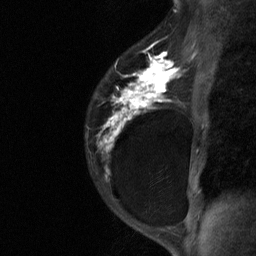
Breast MRI (dynamic contrast-enhanced), one sagittal slice. Slice 47 of 64 in the series (ordered by position). Dynamic contrast-enhanced study with each time point stored as its own series, time point 2 of 3 at this slice position (early post-contrast, ordered by acquisition time). 1.5 T. TE 4.8 ms, TR 27 ms. 2 mm slice thickness. 256 × 256 image matrix, field of view 180 × 180 mm. Female patient, age 34 years. Case-level facts recorded for this patient, not image findings: setting: breast cancer imaged before/during neoadjuvant chemotherapy; receptor status: HR-positive, HER2-negative.
Outlined on this slice (semi-automatic segmentation, software-assisted and operator-edited):
- analysis volume of interest (the breast-tissue region the enhancement analysis was run in; not a lesion): box from (x=85, y=44) to (x=181, y=191) px
- tumour enhancement mask (voxels above the 90 % enhancement threshold inside the analysis volume of interest): (x=99, y=52)–(x=181, y=151)